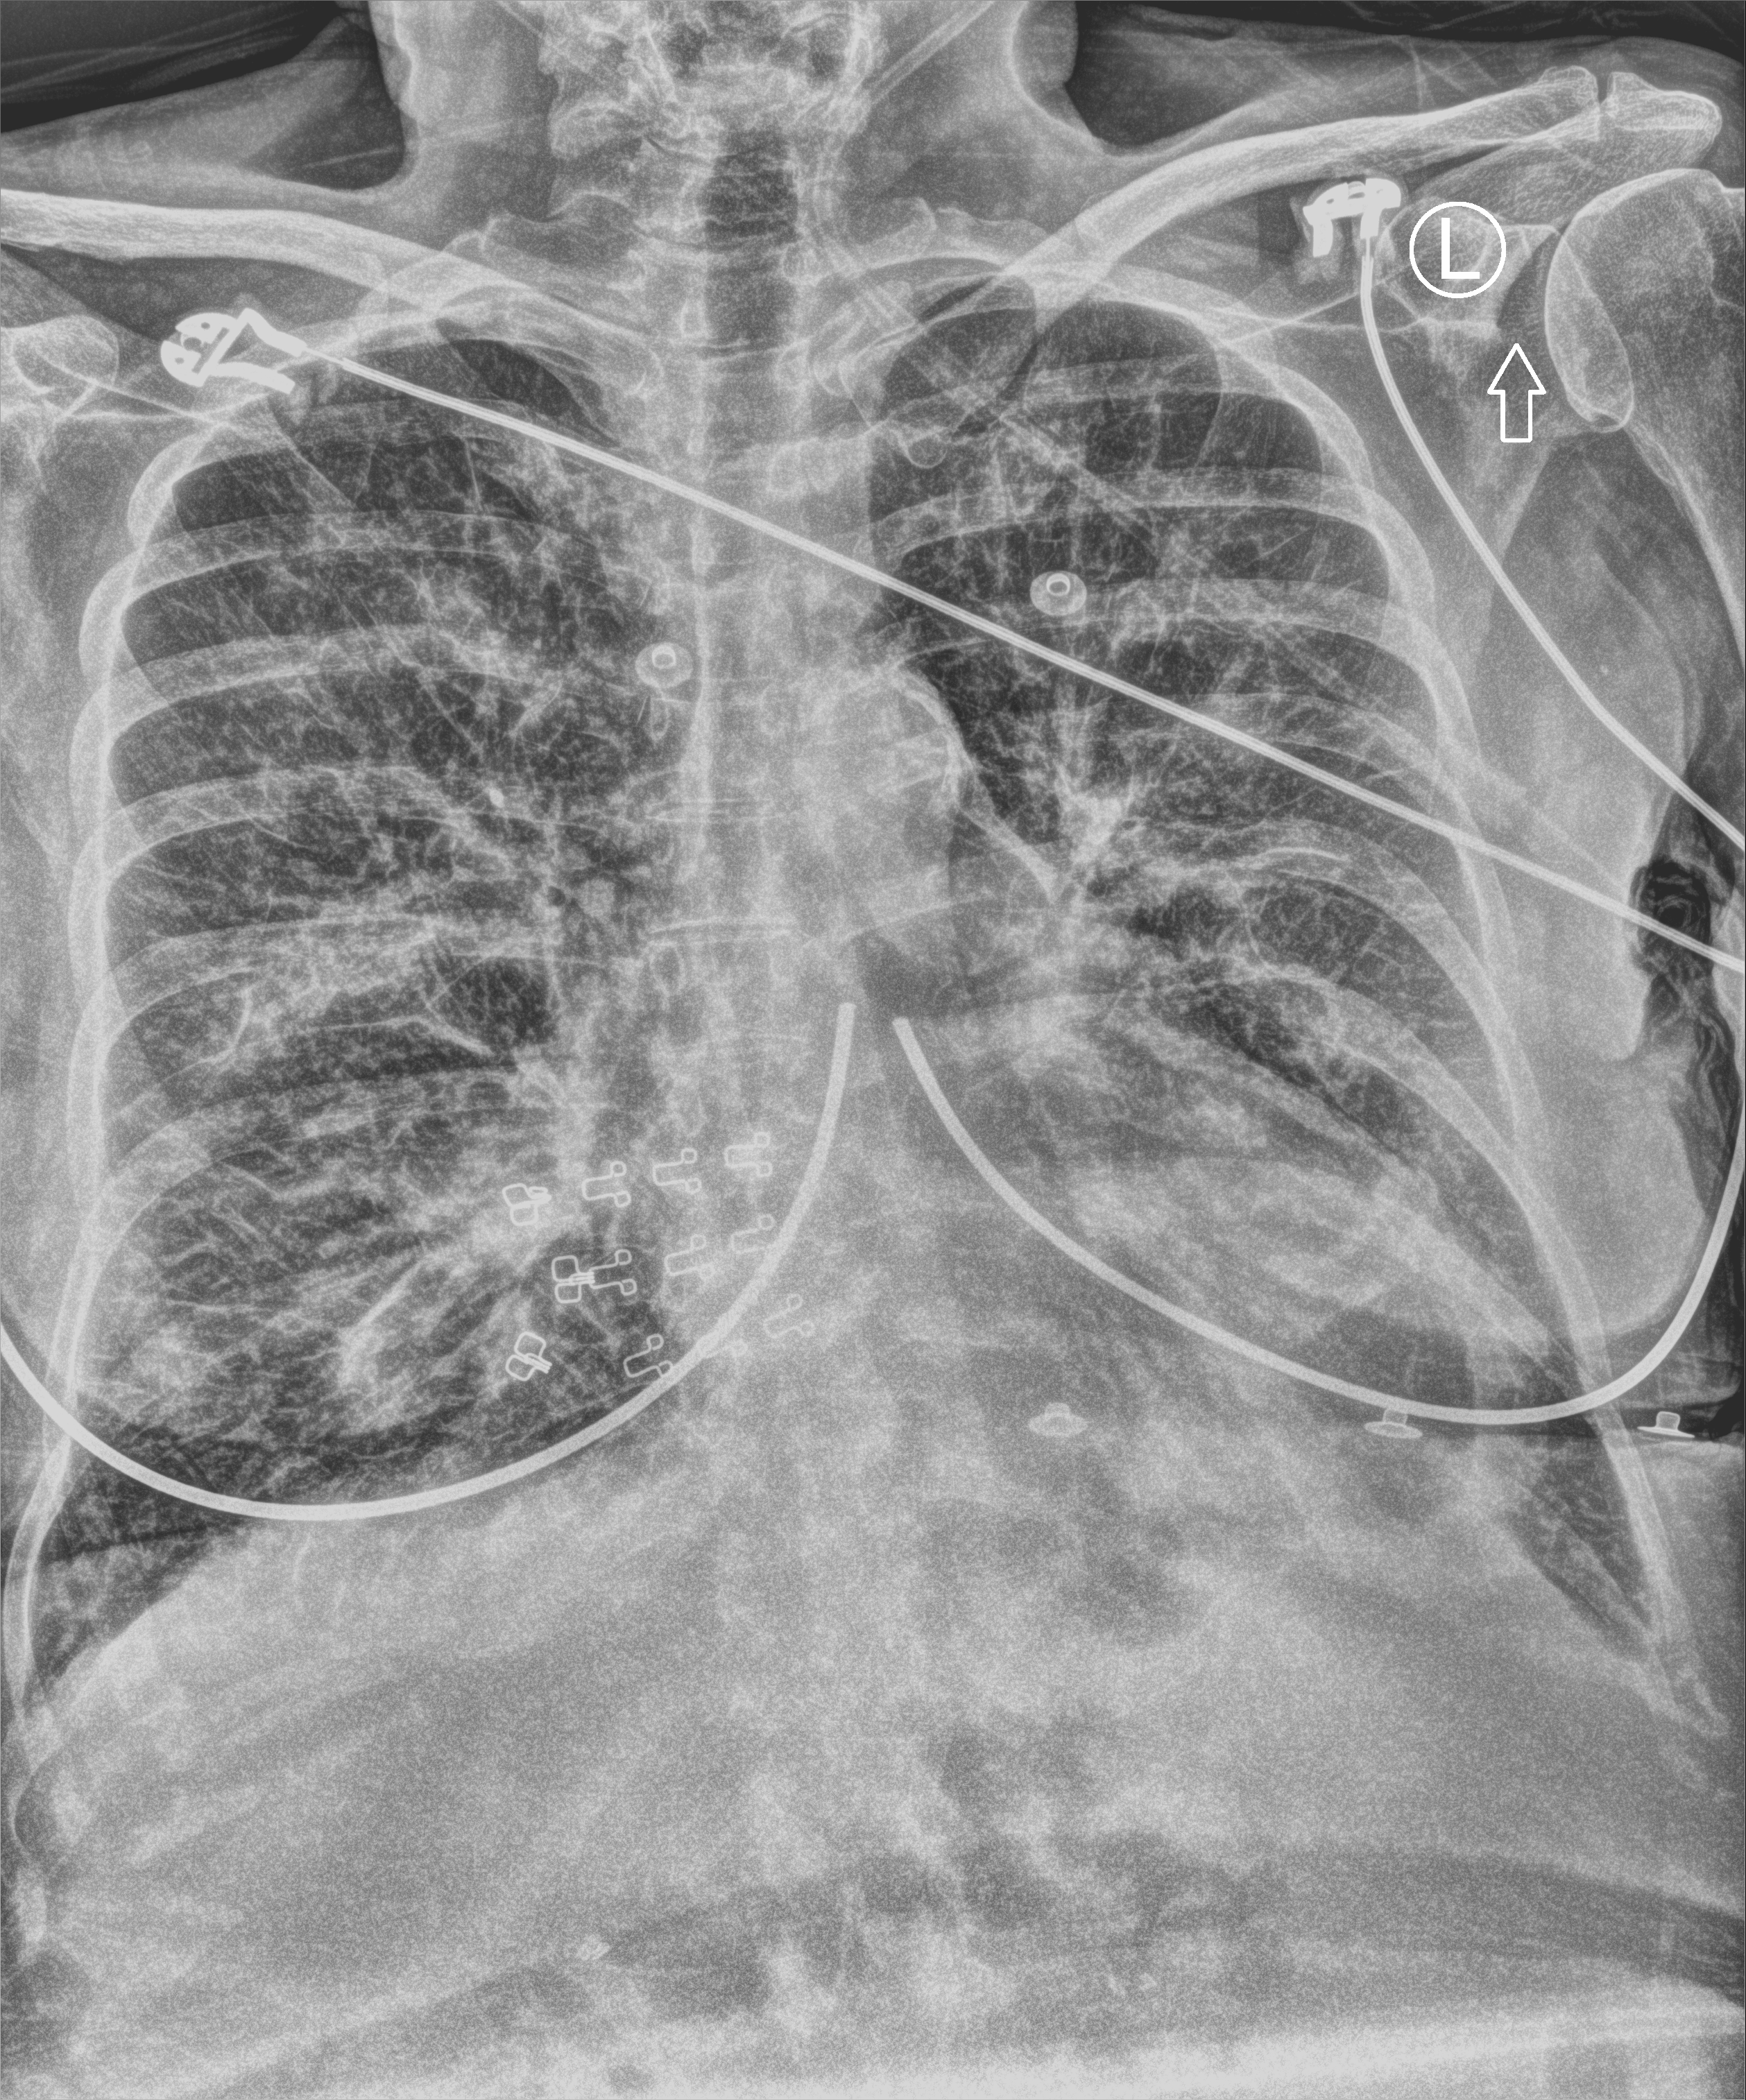
Chest X-ray (portable), anteroposterior (AP) projection. Female patient hospitalised with COVID-19, age 18–59 years.
Hospital-stay facts (about this admission, not read from this image; timing relative to this image not recorded): mechanically ventilated during this hospital stay: no; admitted to intensive care during this hospital stay: no.